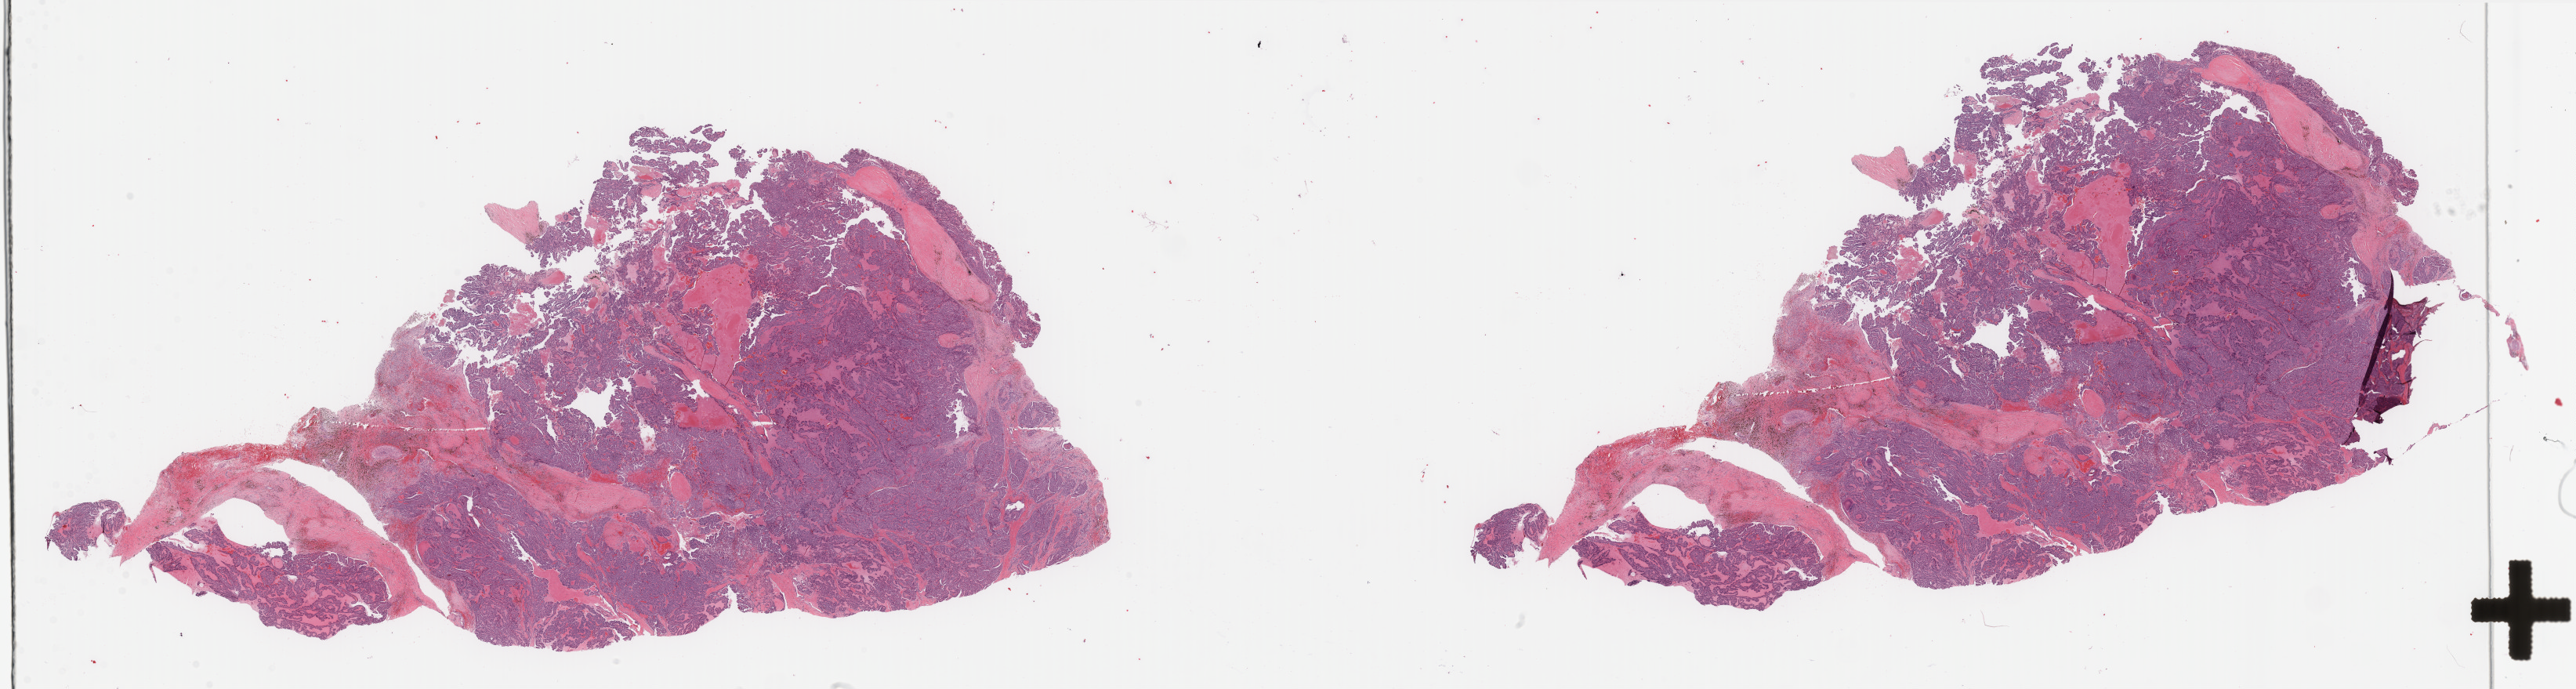
Whole-slide histology image, Hematoxylin and eosin (H&E) stained — a low-resolution overview of the entire scanned area, about 52.0 x 13.9 mm, formalin-fixed paraffin-embedded (FFPE) diagnostic section, sample: primary tumour, thyroid. Male patient; age at initial diagnosis 71 years.
Diagnosis: Papillary adenocarcinoma, NOS (thyroid gland).